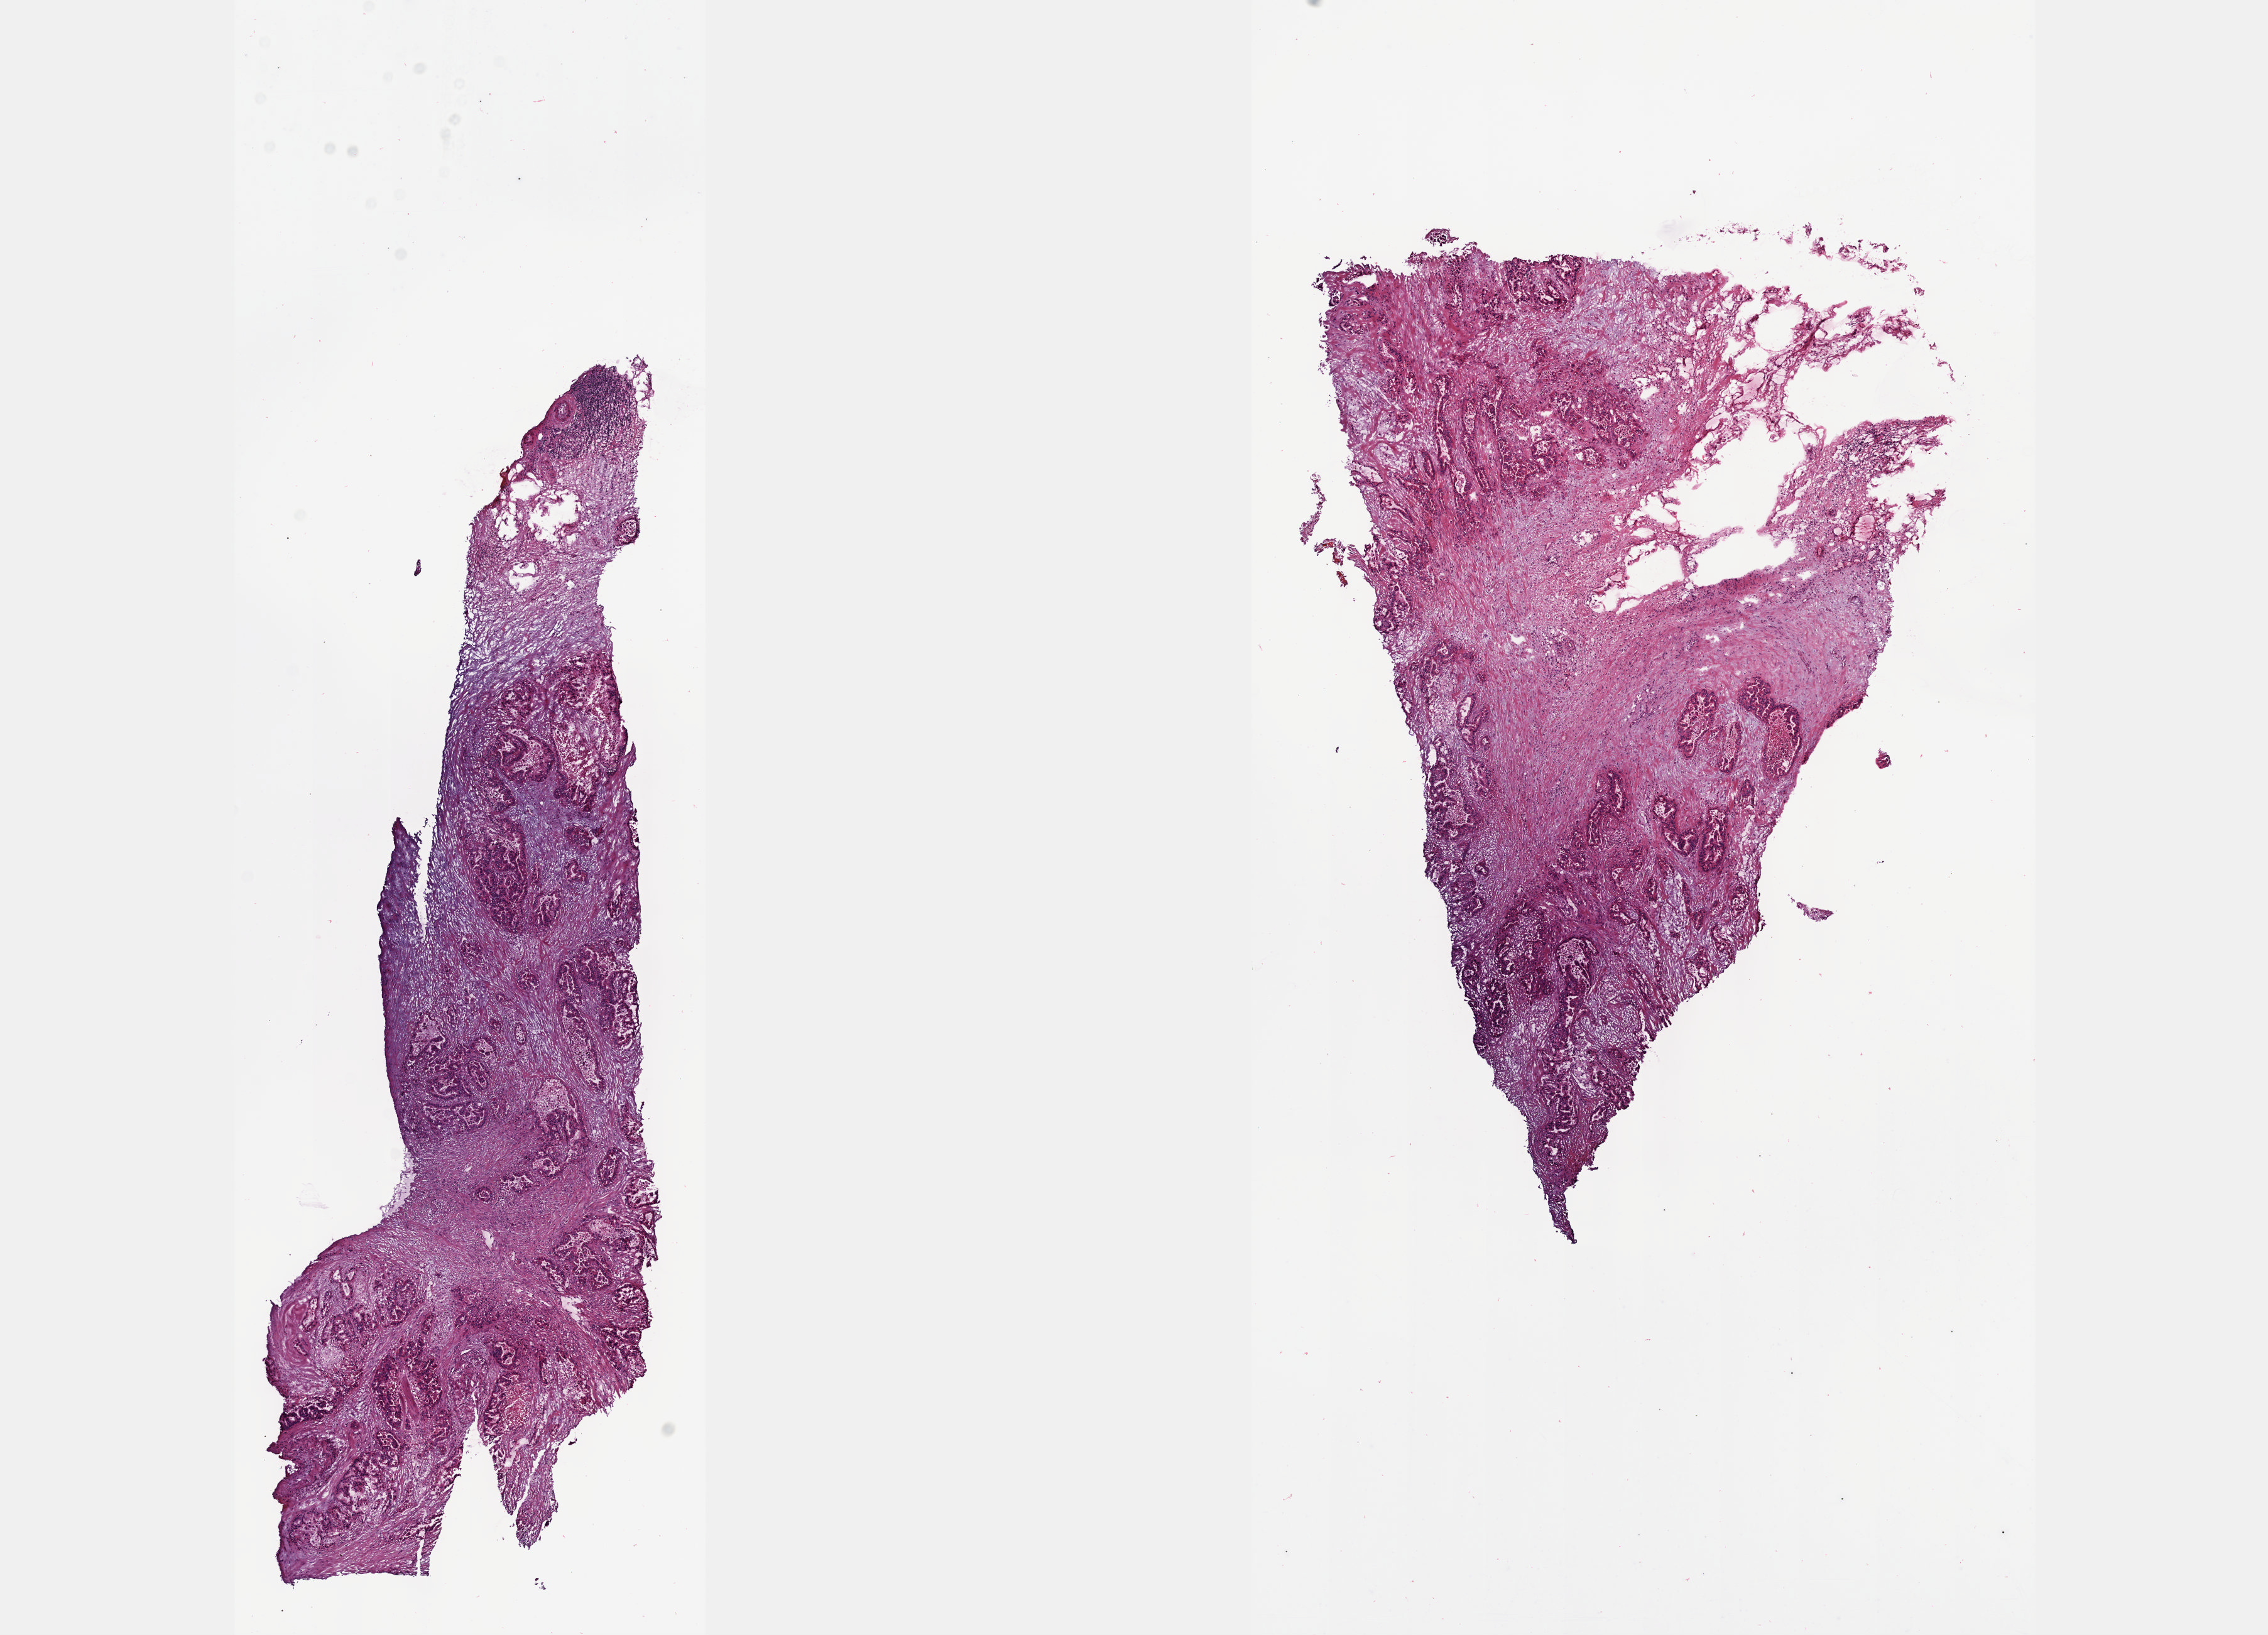
H&E-stained whole-slide image, low-resolution overview of the scanned area, about 14.6 x 10.5 mm (from a 40x scan), frozen section from the top of the tissue portion, primary tumour sample from the pancreas. Male patient; age at initial diagnosis 75 years. Histologic grade: G2 (moderately differentiated). Composition of this section per pathologist review: tumour cells 60%, tumour nuclei 60%, normal cells 0%, stromal cells 35%, necrosis 5%. Inflammatory infiltration, as recorded: lymphocyte infiltration 3%, monocyte infiltration 3%, neutrophil infiltration 5%.
Lymph nodes positive (case pathology): 5 of 14 examined. Histologic diagnosis: Infiltrating duct carcinoma, NOS. AJCC pathologic stage: IIB (7th edition).